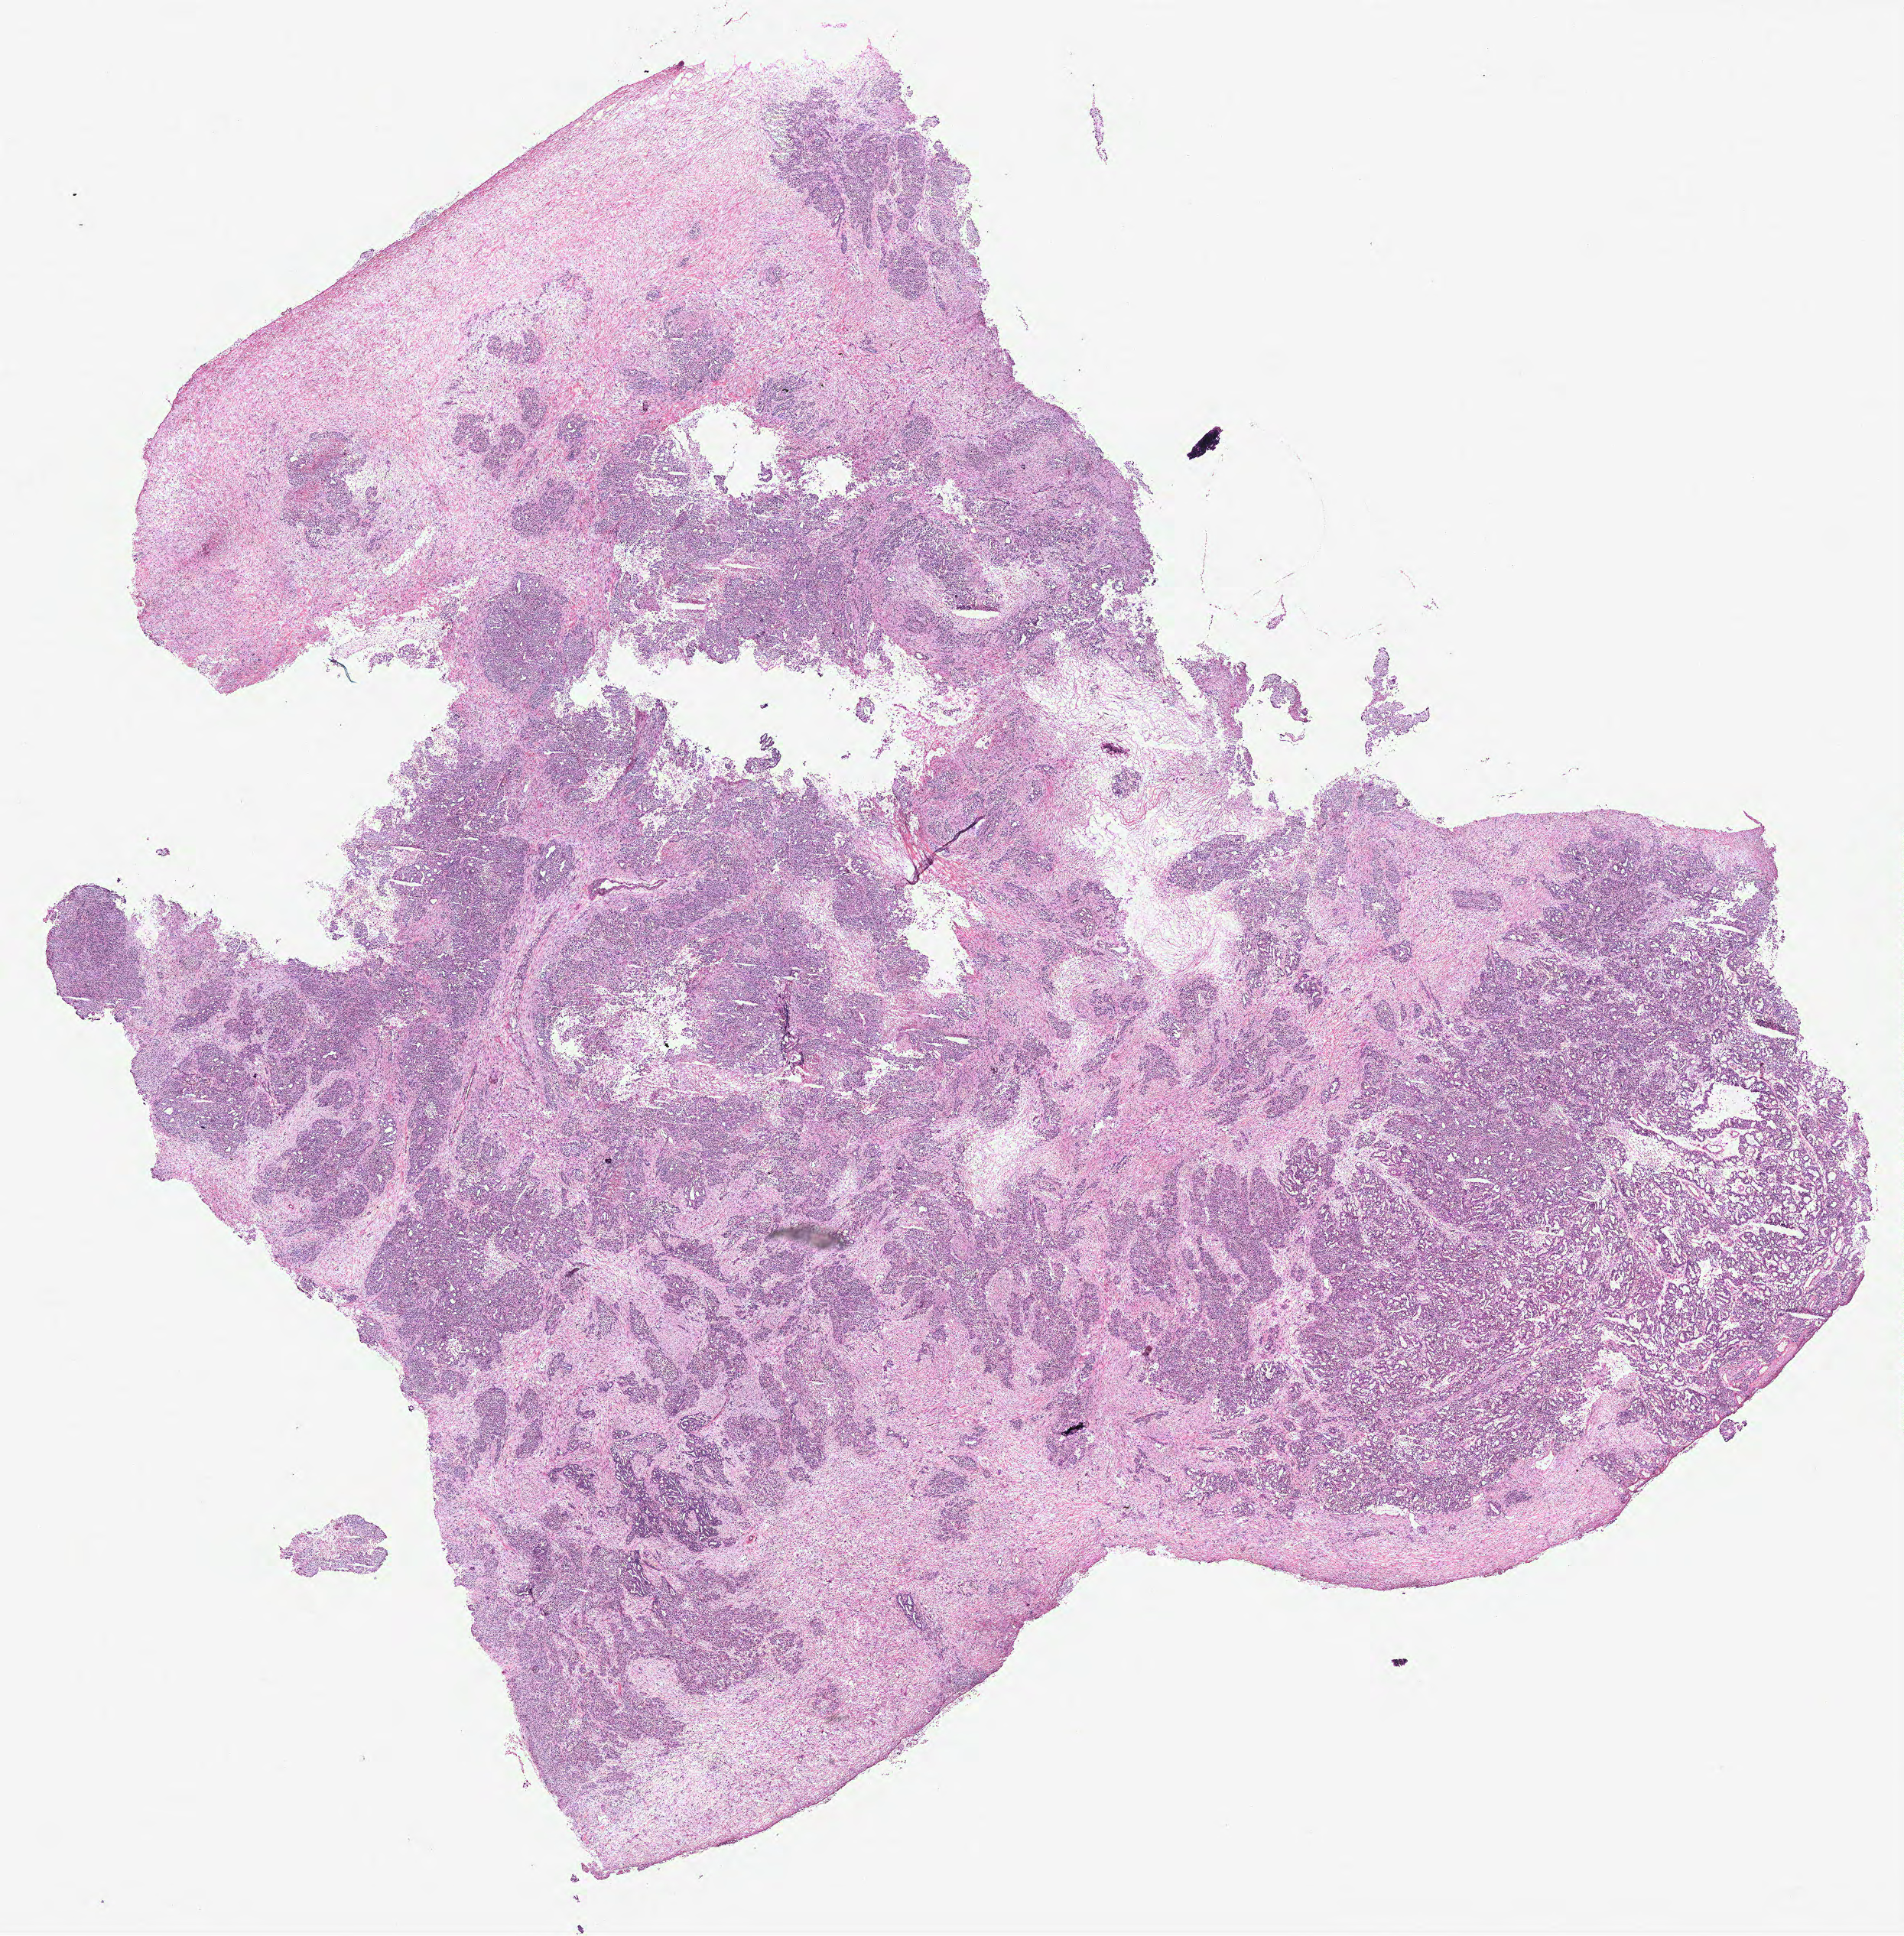
H&E-stained whole-slide image — whole scanned area (about 19.9 x 20.3 mm) shown as a low-resolution overview; ovary, tissue type not recorded. Female patient.
* patient diagnosis: Serous adenocarcinoma, NOS